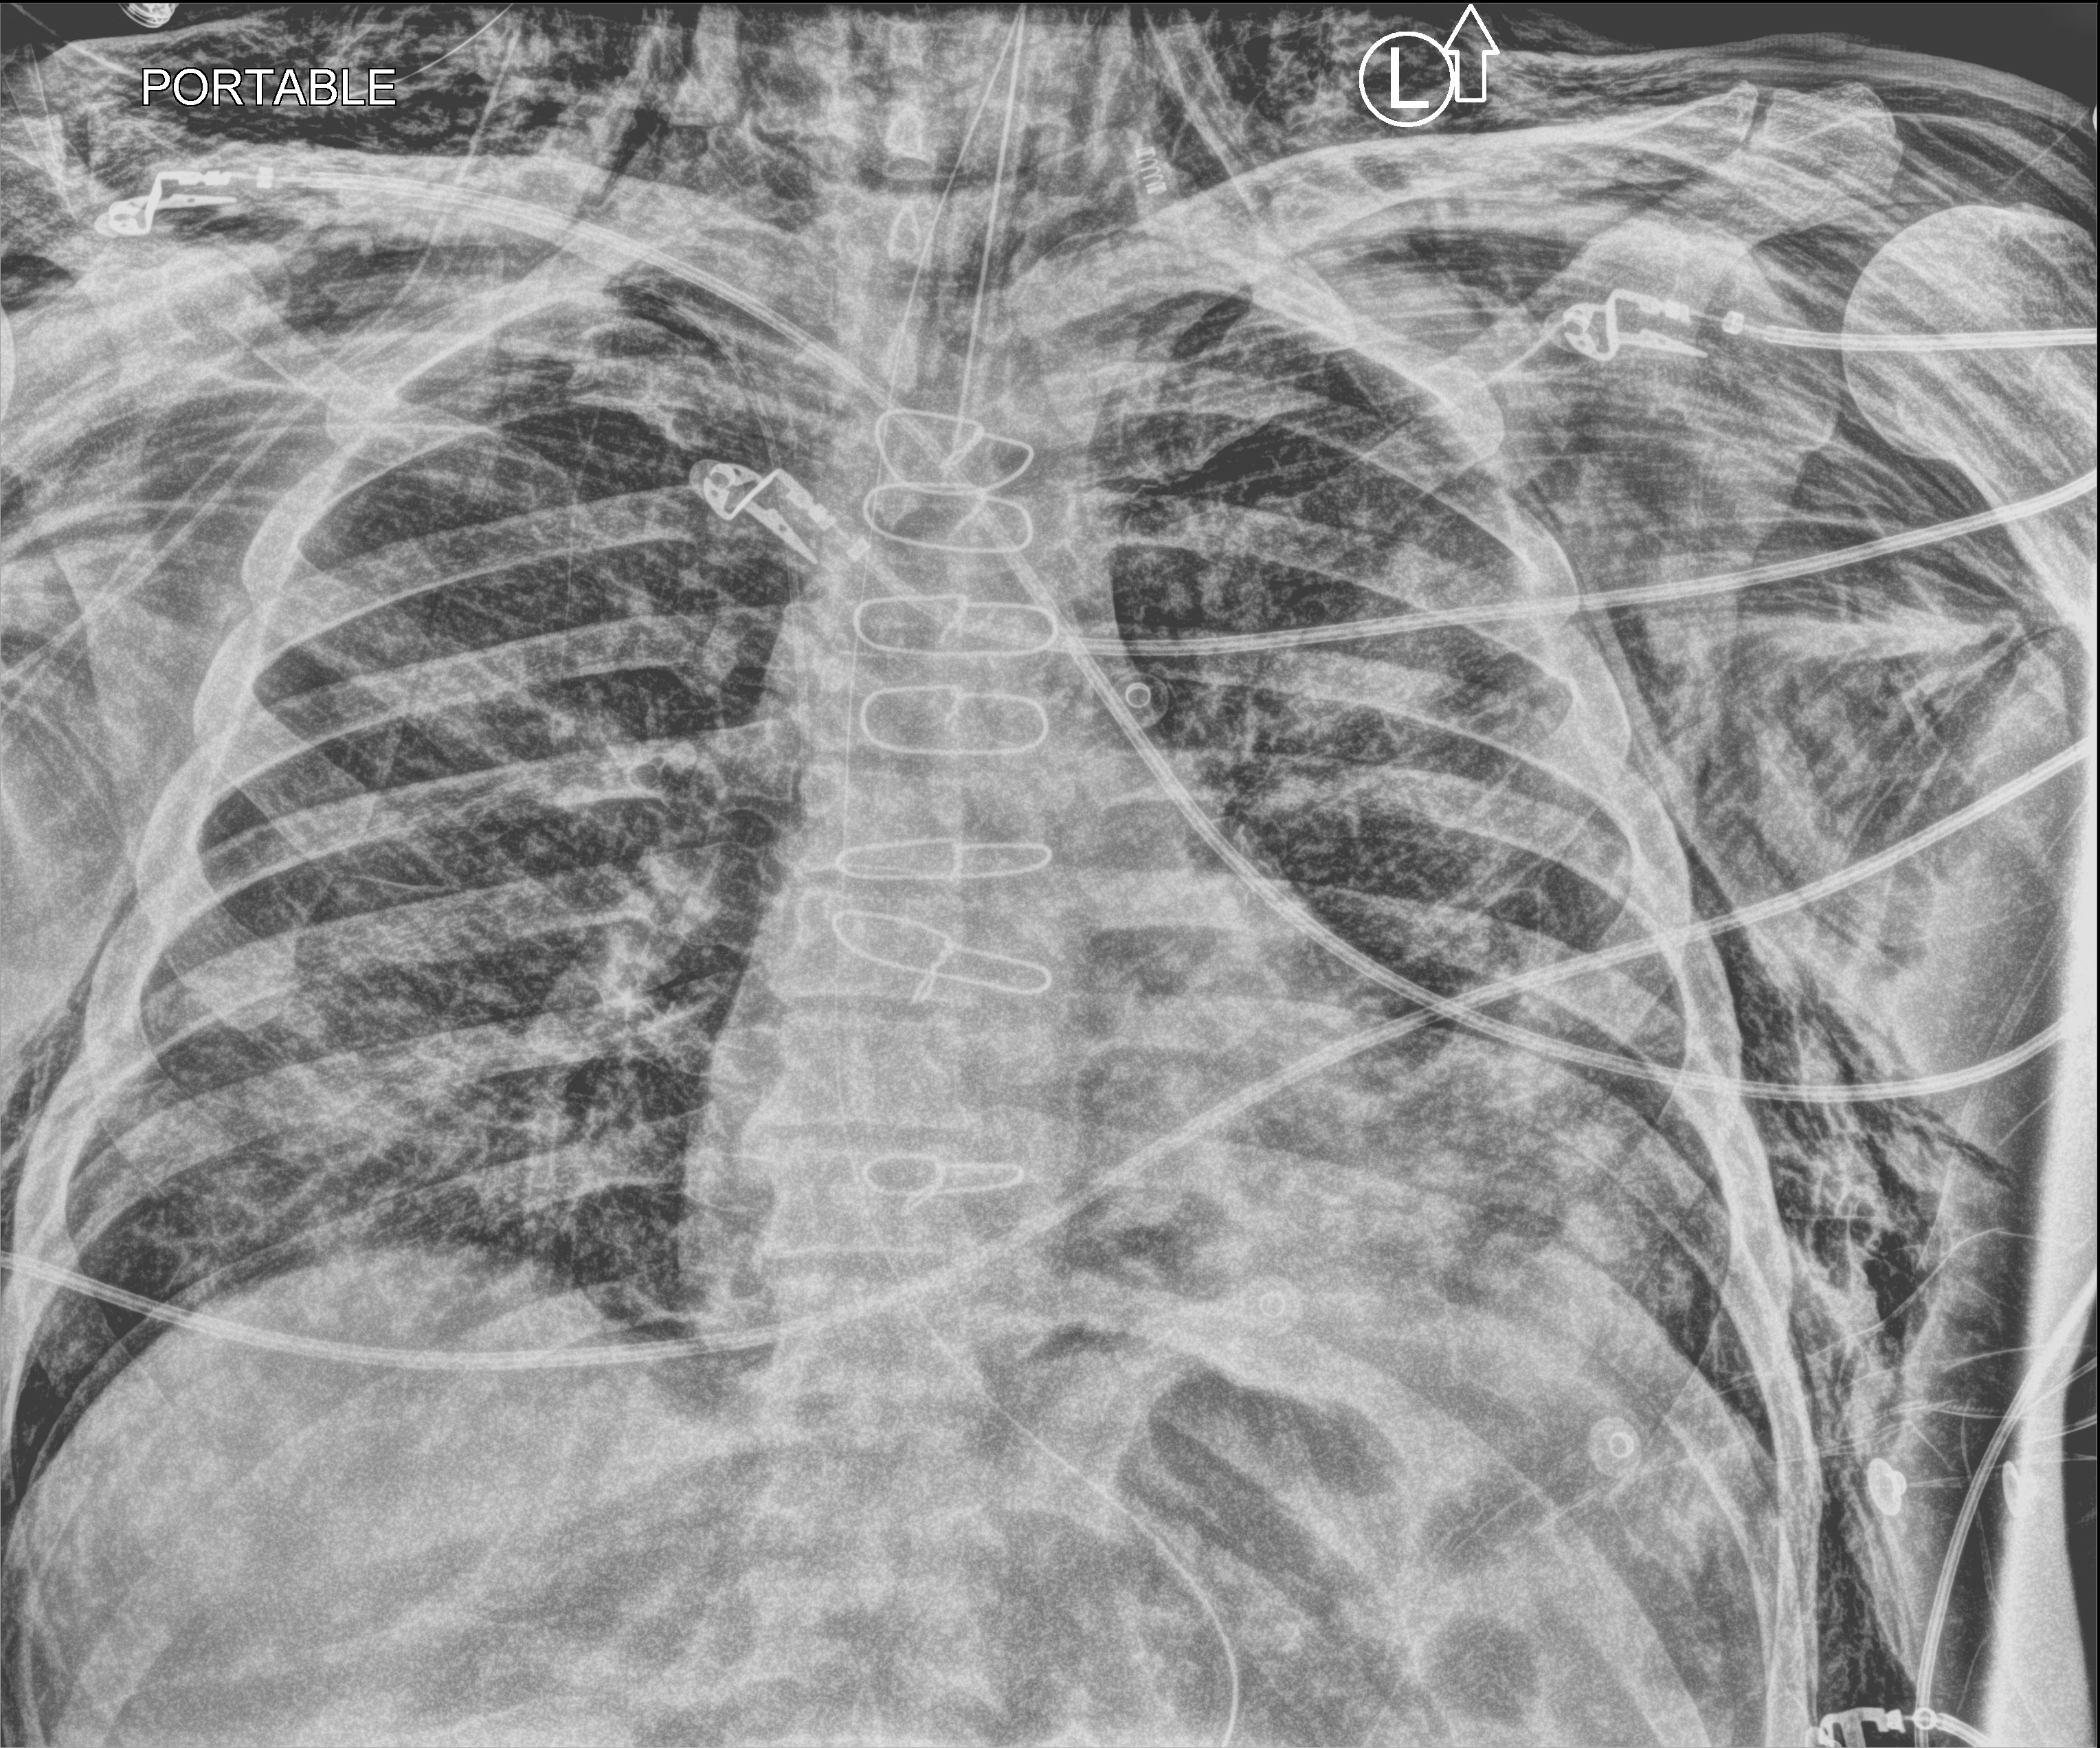
Portable chest radiograph; anteroposterior (AP) projection. Male patient hospitalised with COVID-19, age 60–74 years.
From the hospital-stay record, not from the radiograph (when in the stay this image was taken is not recorded): diabetes (admission record): yes; mechanically ventilated during this hospital stay: yes; other chronic lung disease (admission record): no.